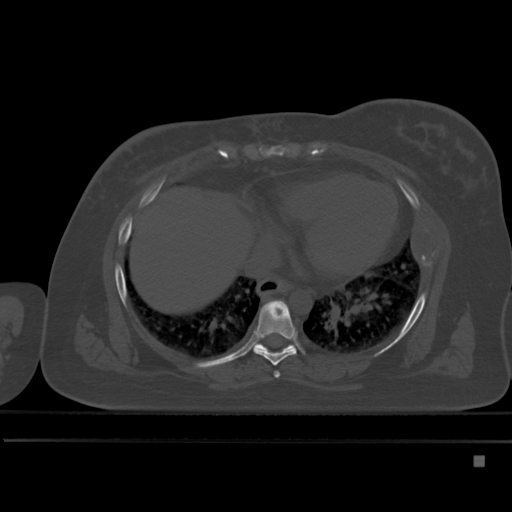
CT including the spine, one axial slice; slice 288 of 495 in the series (ordered by position); bone window (W 1800 / L 400 HU); 1.5 mm slice thickness; 512 × 512 image matrix, field of view 404 × 404 mm. Patient: female, 33 years. Case-level facts recorded for this patient, not image findings: primary cancer: breast; vertebrae with lytic lesions (as recorded): T1.
Structures marked on this image (semi-automatically segmented with operator editing):
- T6 vertebra: bounding box [x1, y1, x2, y2] px = [274, 371, 280, 378]
- T7 vertebra: [253, 300, 297, 366]
- T8 vertebra: [252, 341, 296, 351]